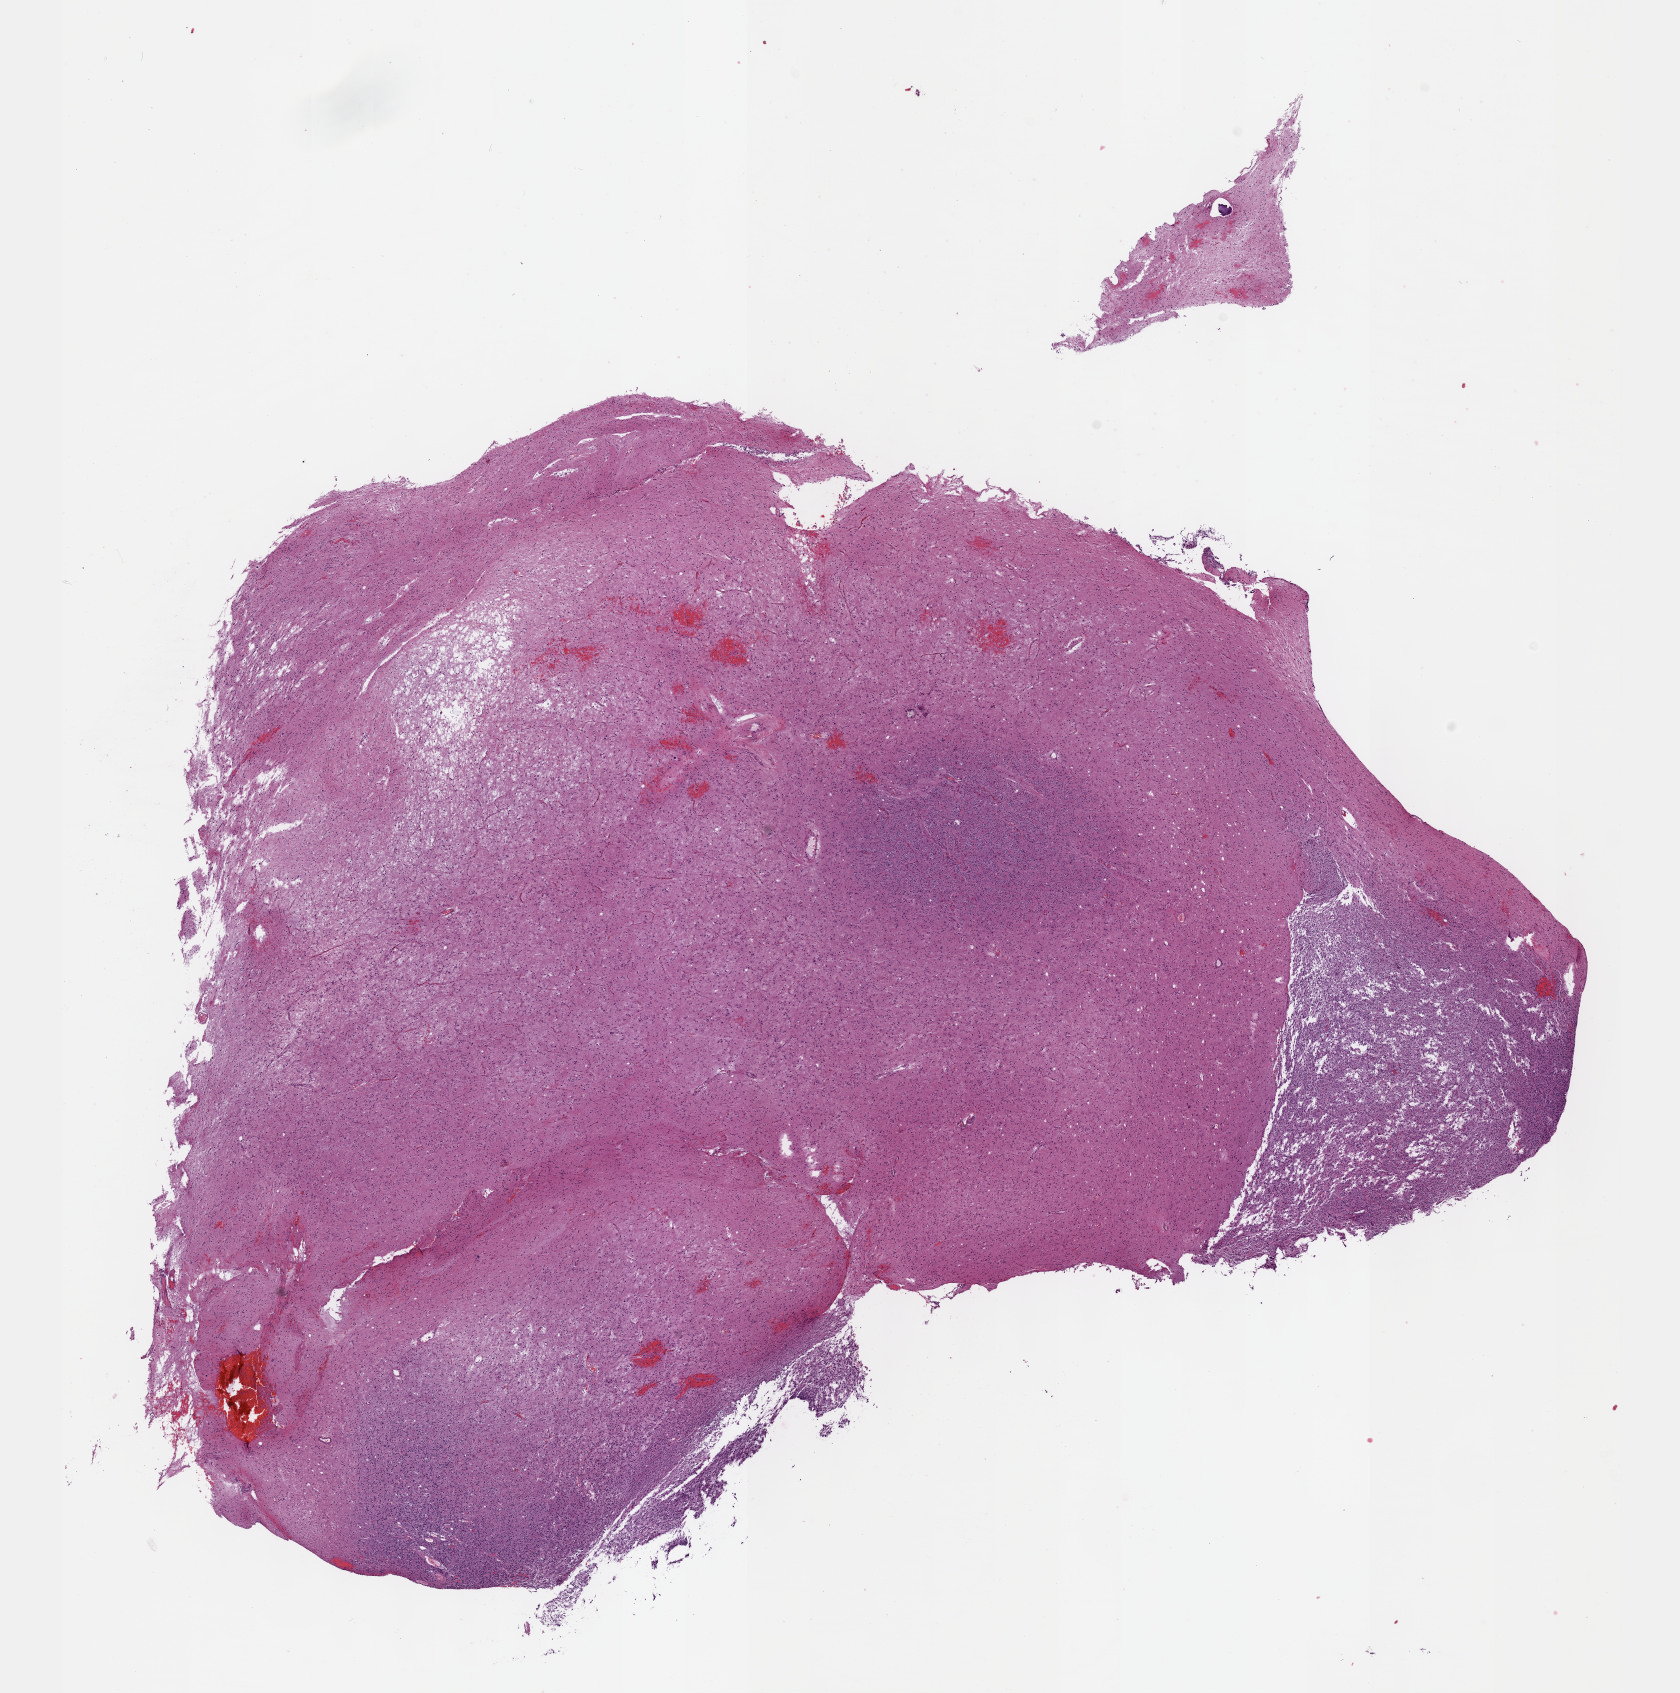
Hematoxylin and eosin (H&E) stained whole-slide image — low-resolution overview of the scanned area, about 13.6 x 13.7 mm (slide scanned at 40x). Formalin-fixed paraffin-embedded (FFPE) diagnostic section. Sample: primary tumour, brain. Male, age 60 years at initial diagnosis.
Diagnosis: Oligodendroglioma, anaplastic.